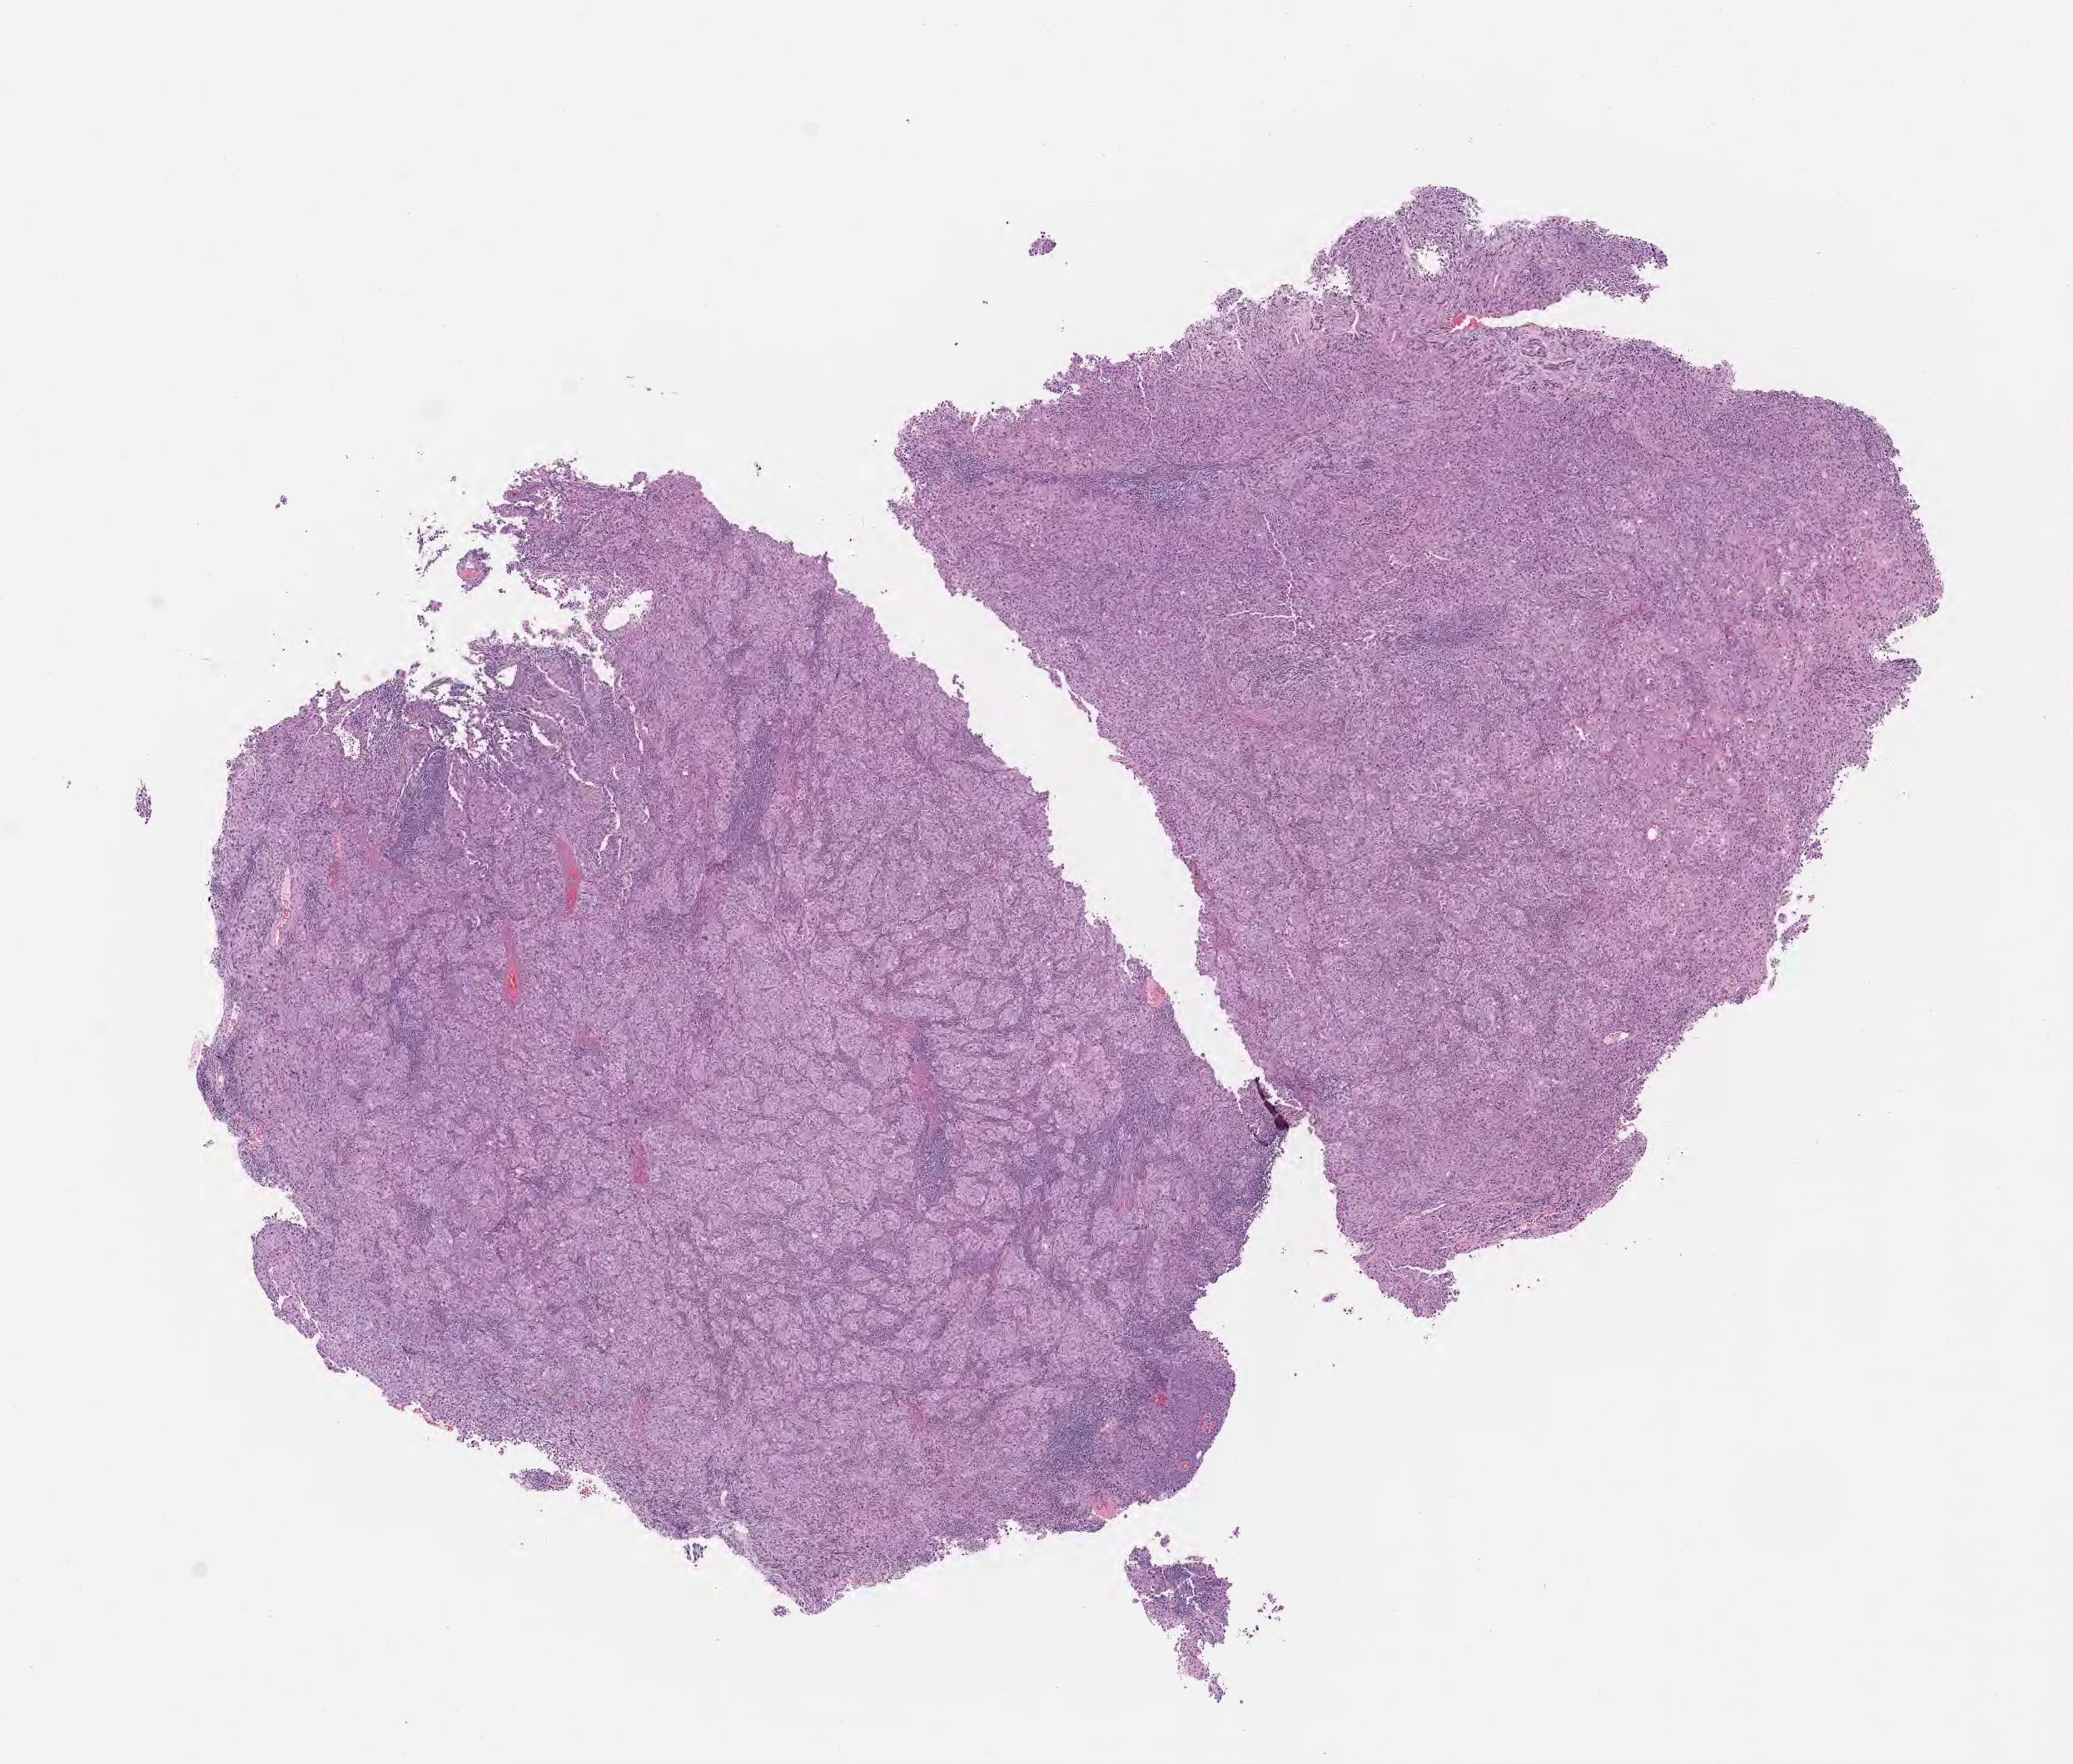
Digitized H&E-stained section — shown as a low-resolution overview of the whole scanned area (about 10.1 x 8.6 mm), specimen: tumor tissue, site: cervix. Patient female; 42 years old.
Histologic diagnosis: Neoplasm, uncertain whether benign or malignant.